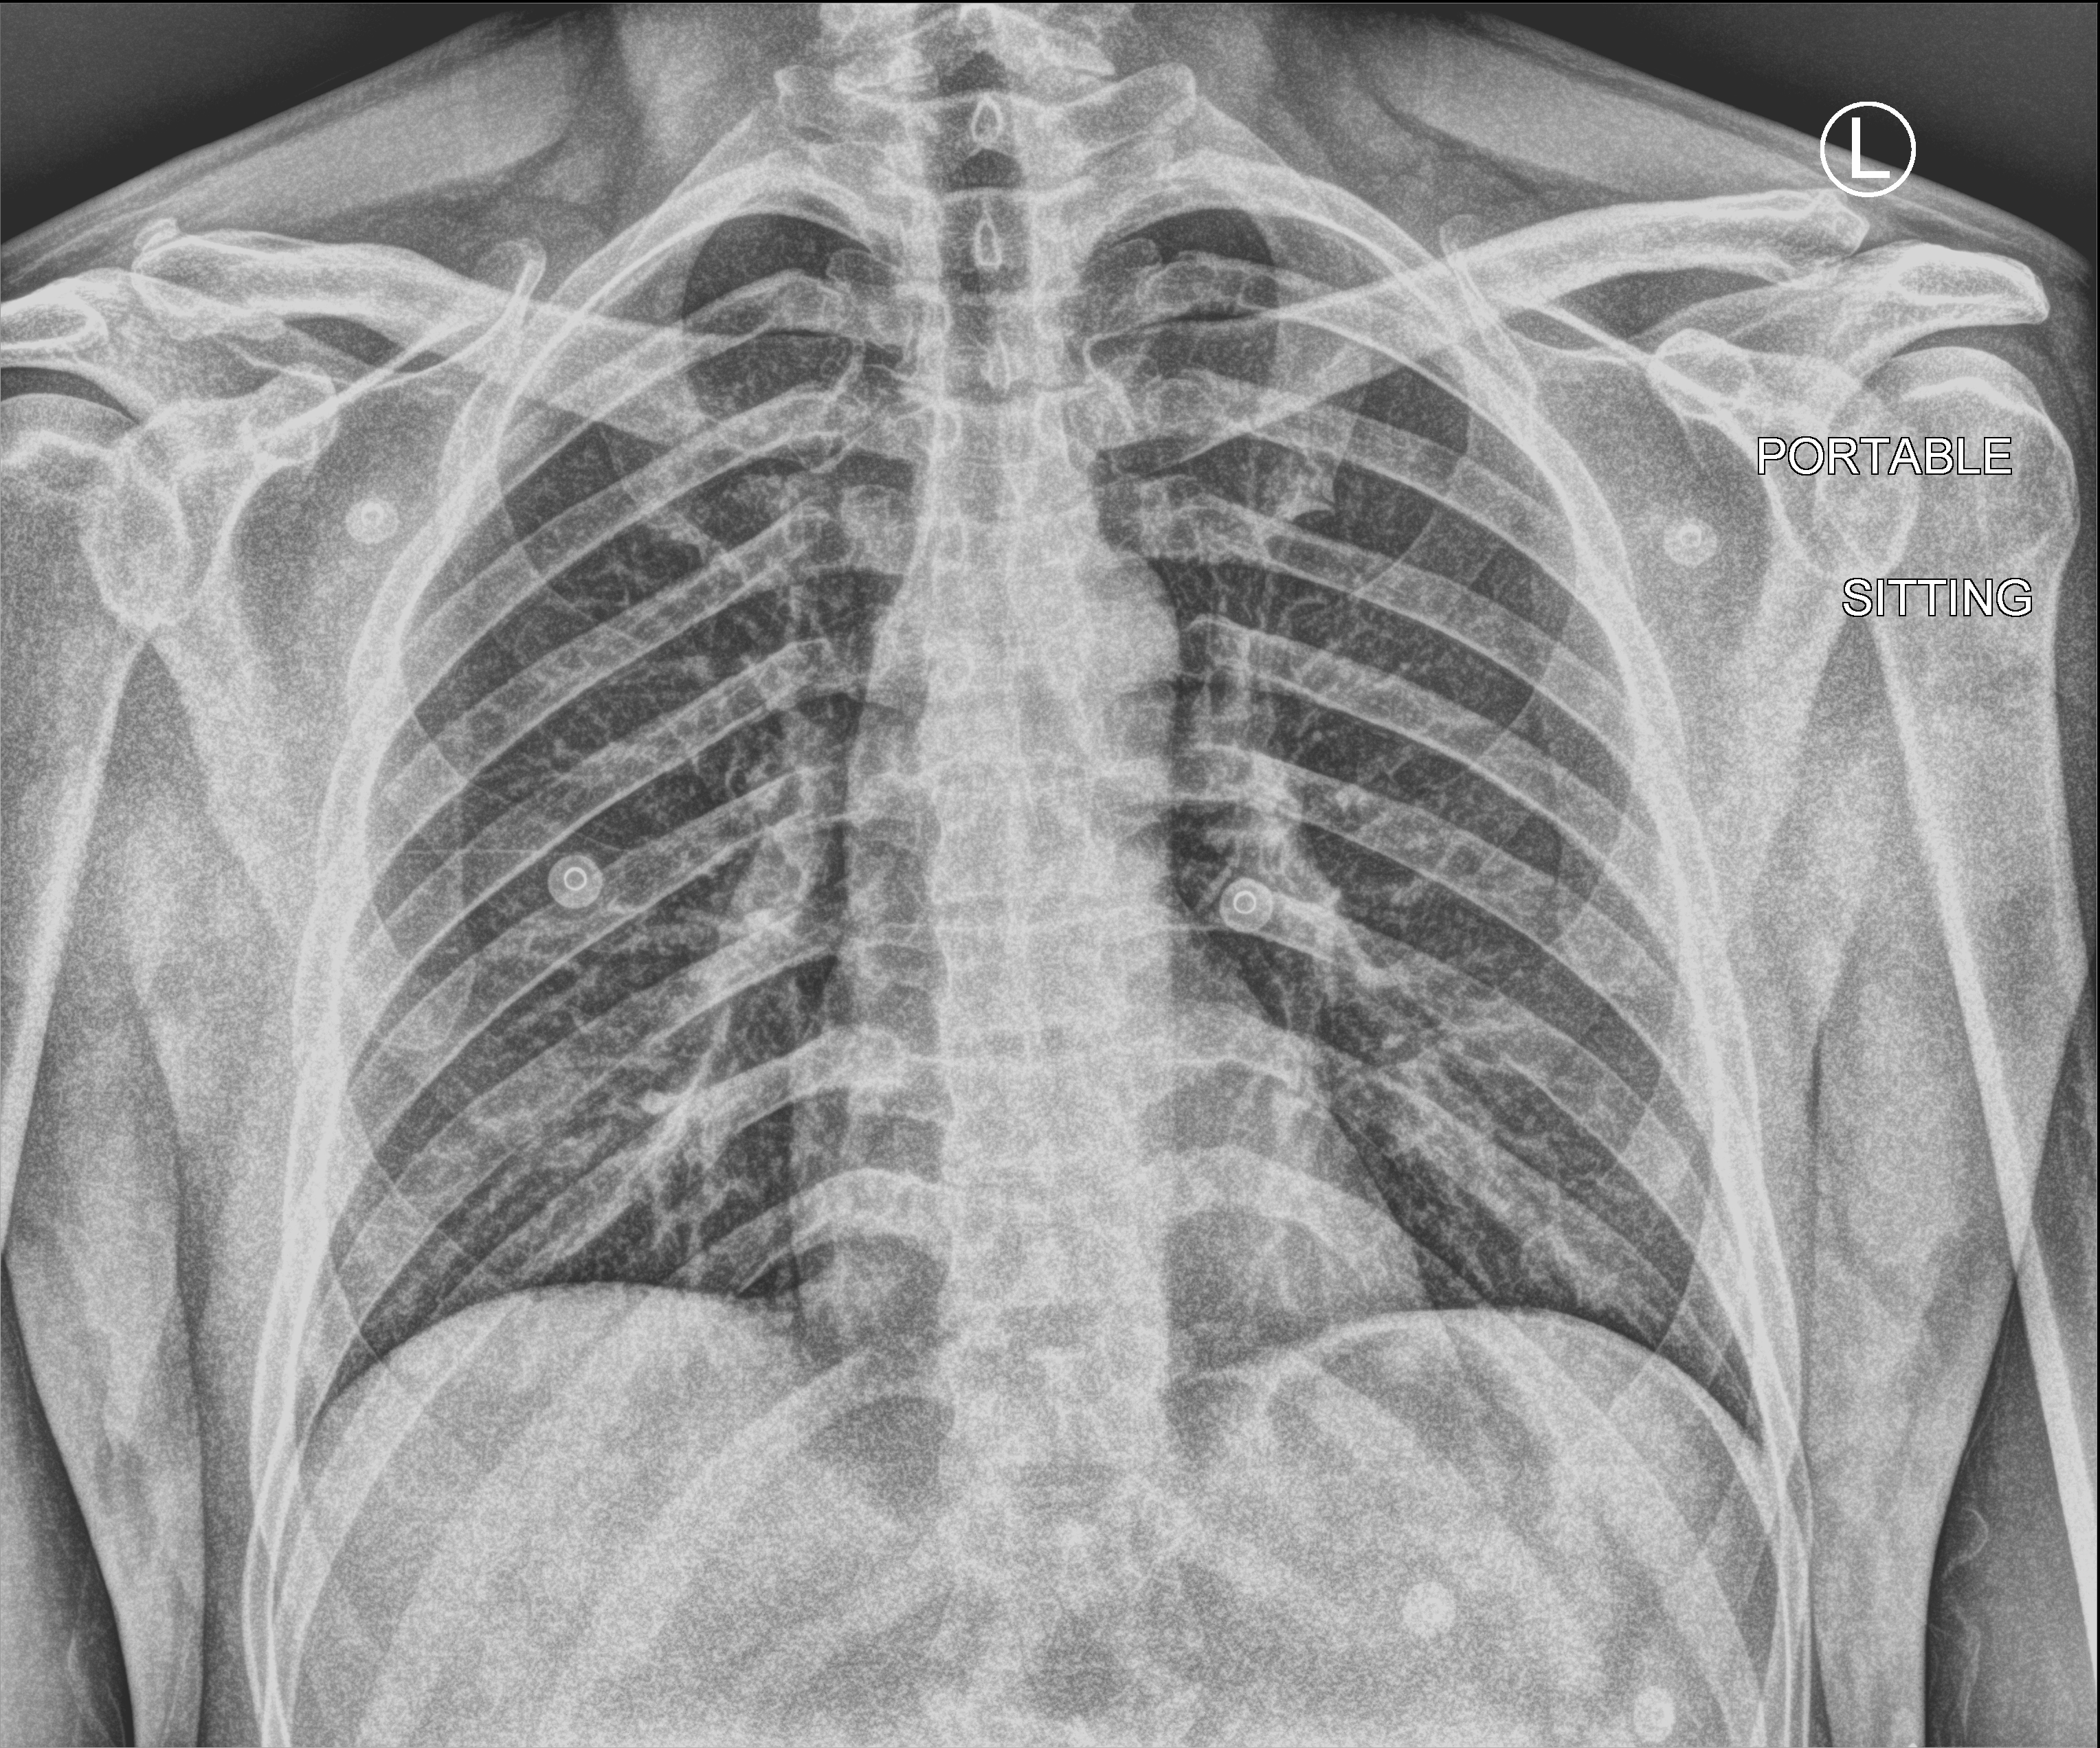
Portable chest radiograph. Patient hospitalised with COVID-19; male, aged 18–59 years.
Admission-level facts for this patient (not findings on this image; timing relative to this image not recorded): length of hospital stay: 1 day; COPD (admission record): no.